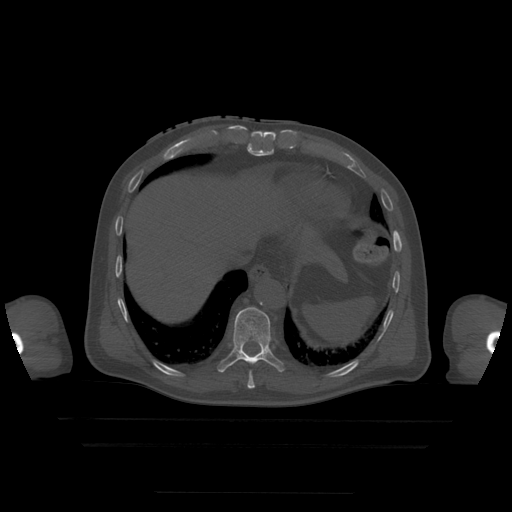
CT including the spine, one axial slice; position 244 of 522 along the scan axis; bone window (W 1800 / L 400 HU); 1.25 mm slice thickness; 512 × 512 image matrix, field of view 436 × 436 mm. Patient age 68 years. Case-level facts recorded for this patient, not image findings: primary cancer: urothelial.
Outlined on this slice (semi-automatic segmentation, software-assisted and operator-edited):
- T10 vertebra: bounding box (x1, y1, x2, y2) in pixels: (218, 307, 286, 373)
- T9 vertebra: (247, 372, 255, 389)